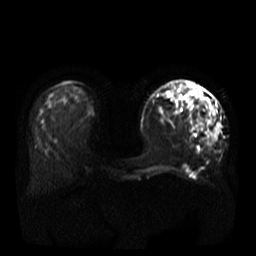
Breast MRI, one axial slice. Slice 12 of 37 in the series (ordered by position). Diffusion-weighted series; image 2 of 4 stored at this slice position (different b-values; order by instance number). 3 T. 5 mm slice thickness. 256 × 256 image matrix, field of view 380 × 380 mm. Female patient.
Structures marked on this image (expert manual segmentation):
- tumour on diffusion-weighted imaging: box from (x=200, y=97) to (x=221, y=143) px